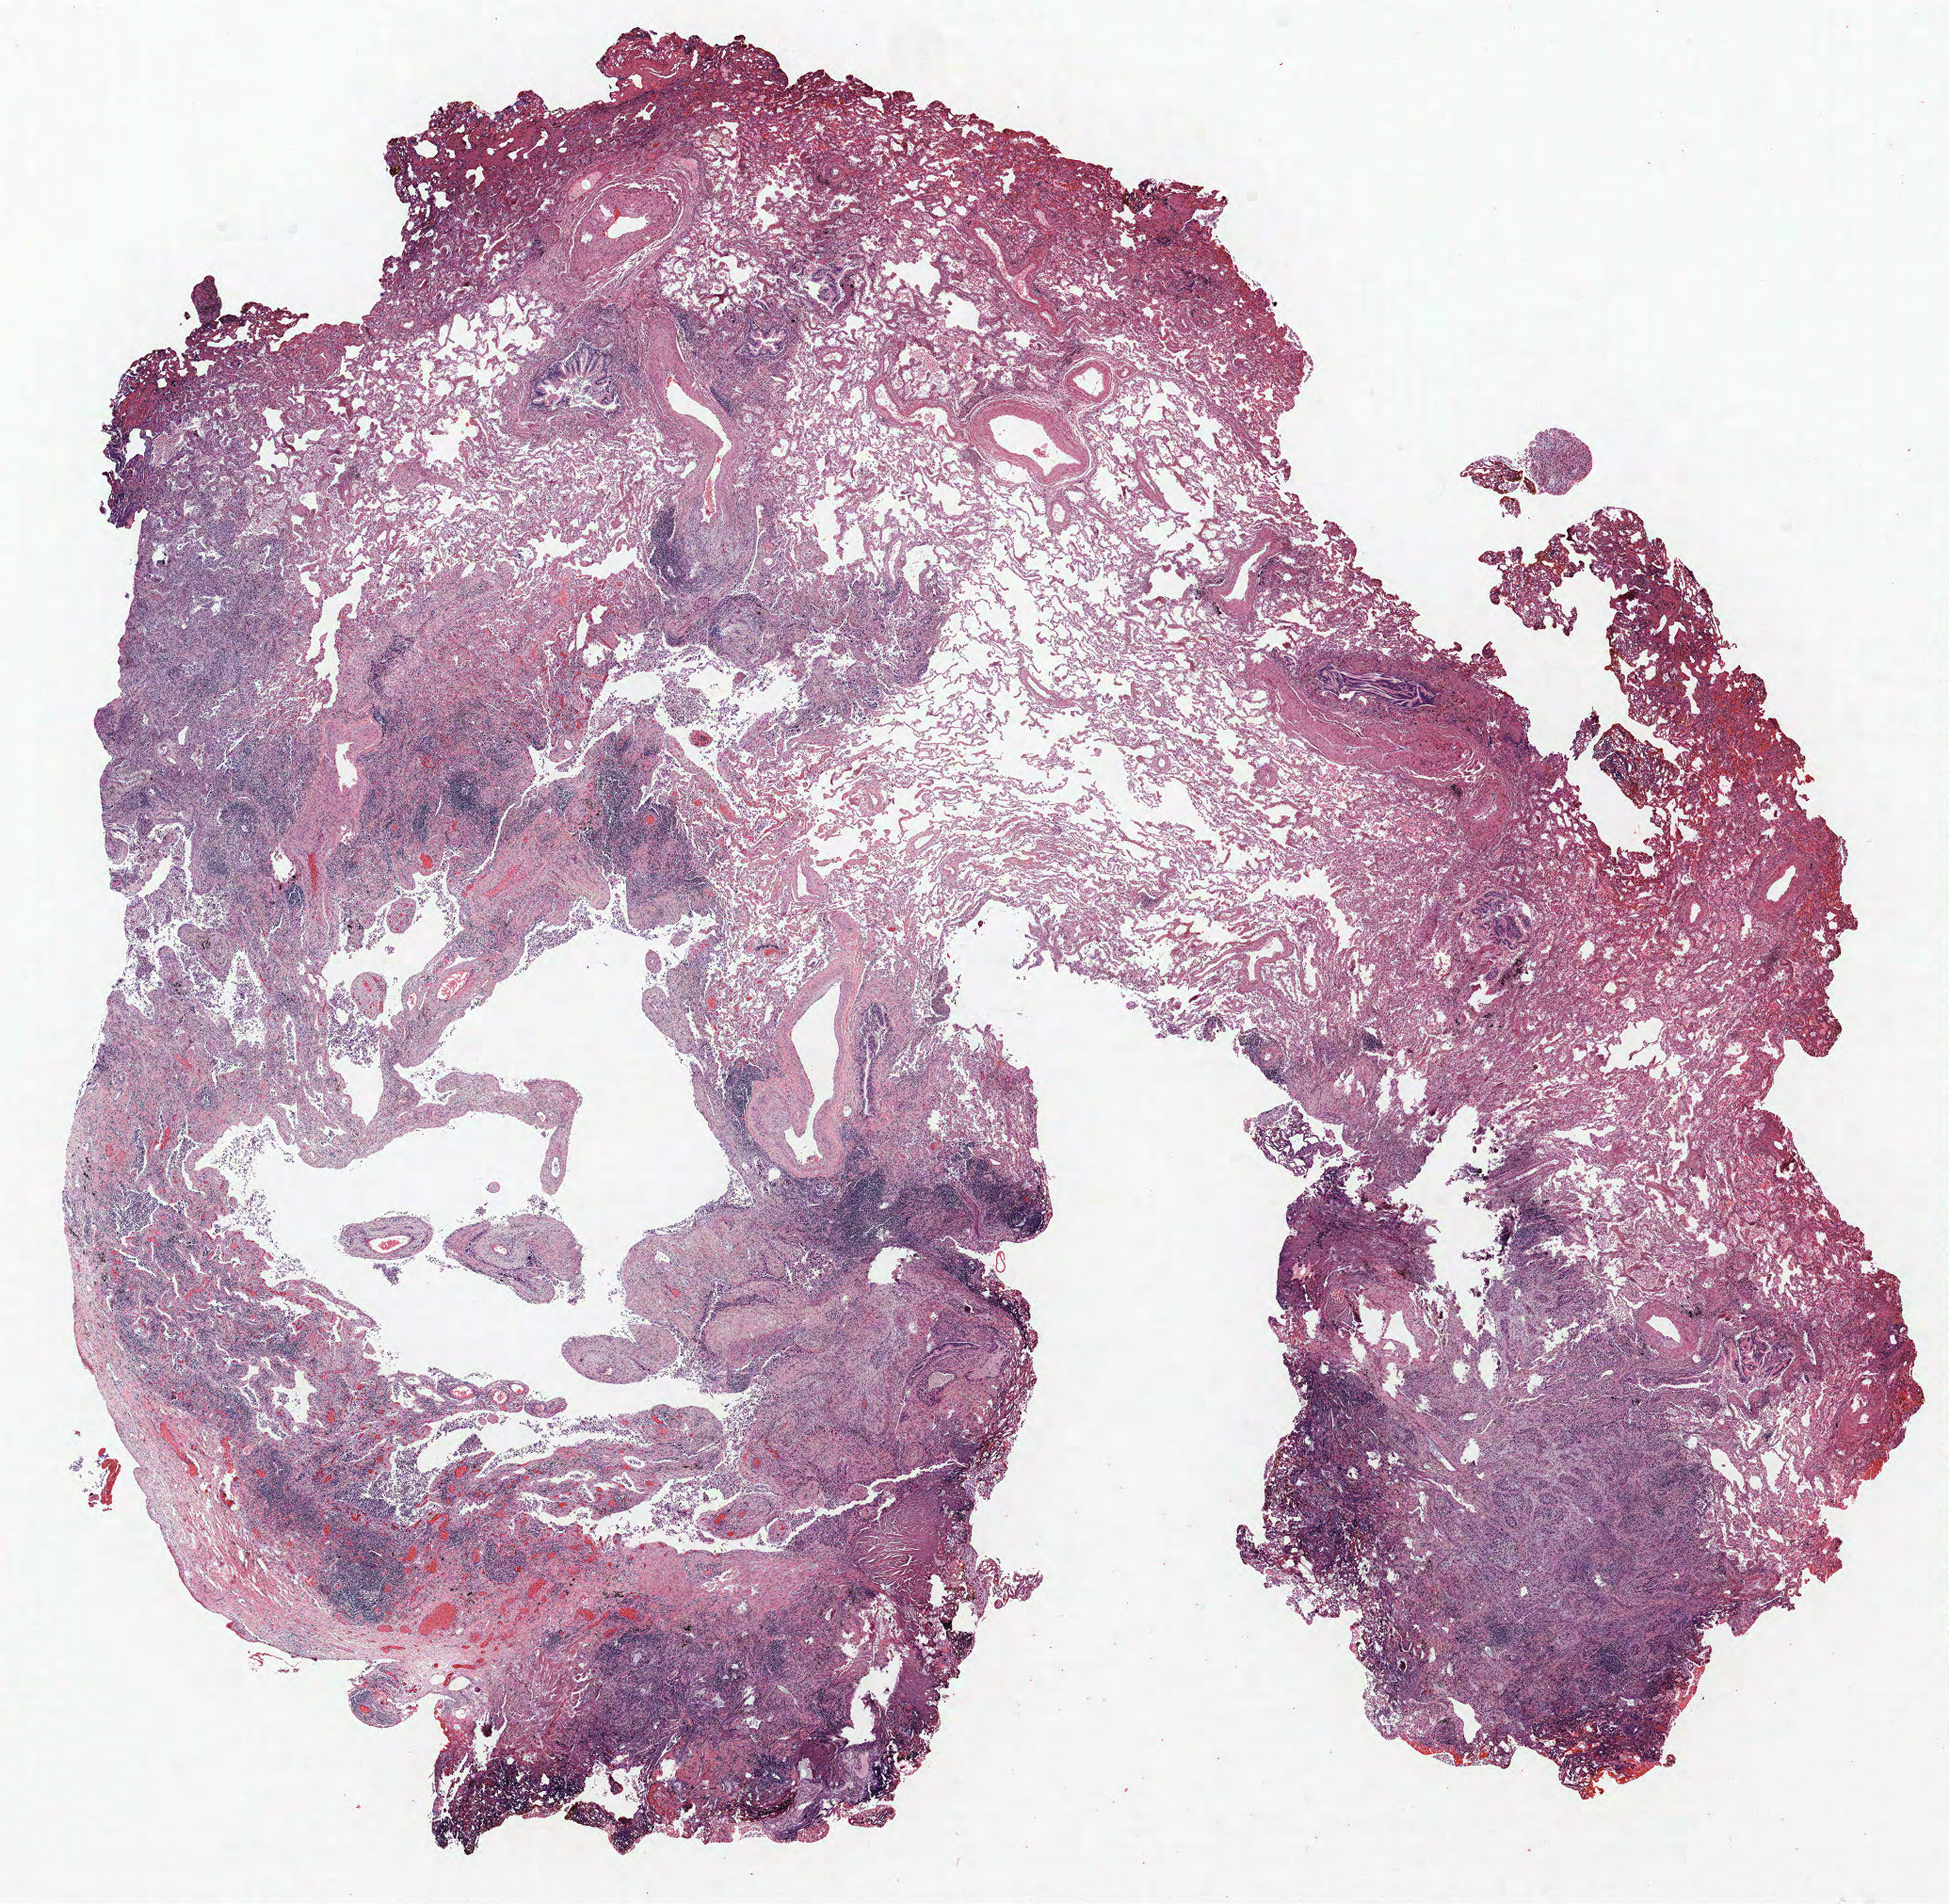
H&E whole-slide image, whole scanned area (about 16.6 x 16.2 mm, acquisition: 40x scan) shown as a low-resolution overview, formalin-fixed paraffin-embedded (FFPE) section, lung. Male patient, aged 59 at enrolment. Current smoker at enrolment. Grade: moderately differentiated (G2).
* participant's lung-cancer diagnosis: Adenocarcinoma, NOS
* tumour size (pathology): 13 mm
* stage (AJCC 6th edition): IA
* primary tumour location (clinical record): right upper lobe, right middle lobe
* note: participant had 2 primary lung cancers recorded; fields above describe the first